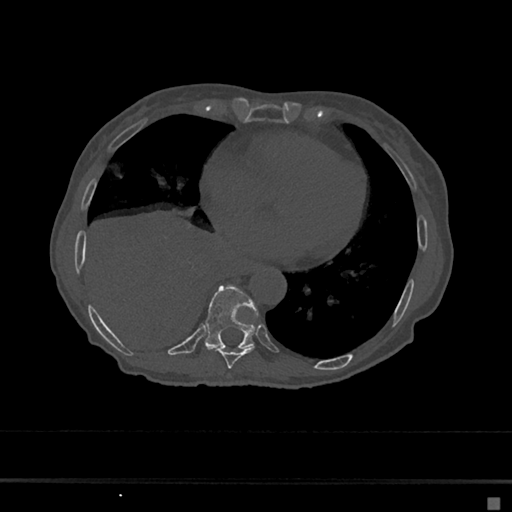
CT including the spine, one axial slice; position 297 of 797 along the scan axis; 120 kVp; bone window (W 1800 / L 400 HU); 512 × 512 image matrix, field of view 360 × 360 mm. Patient: female, 68 years. Case-level facts recorded for this patient, not image findings: primary cancer: renal.
Structures marked on this image (semi-automatically segmented with operator editing):
- T8 vertebra: bounding box [x1, y1, x2, y2] px = [214, 347, 255, 369]
- T9 vertebra: [203, 285, 258, 349]